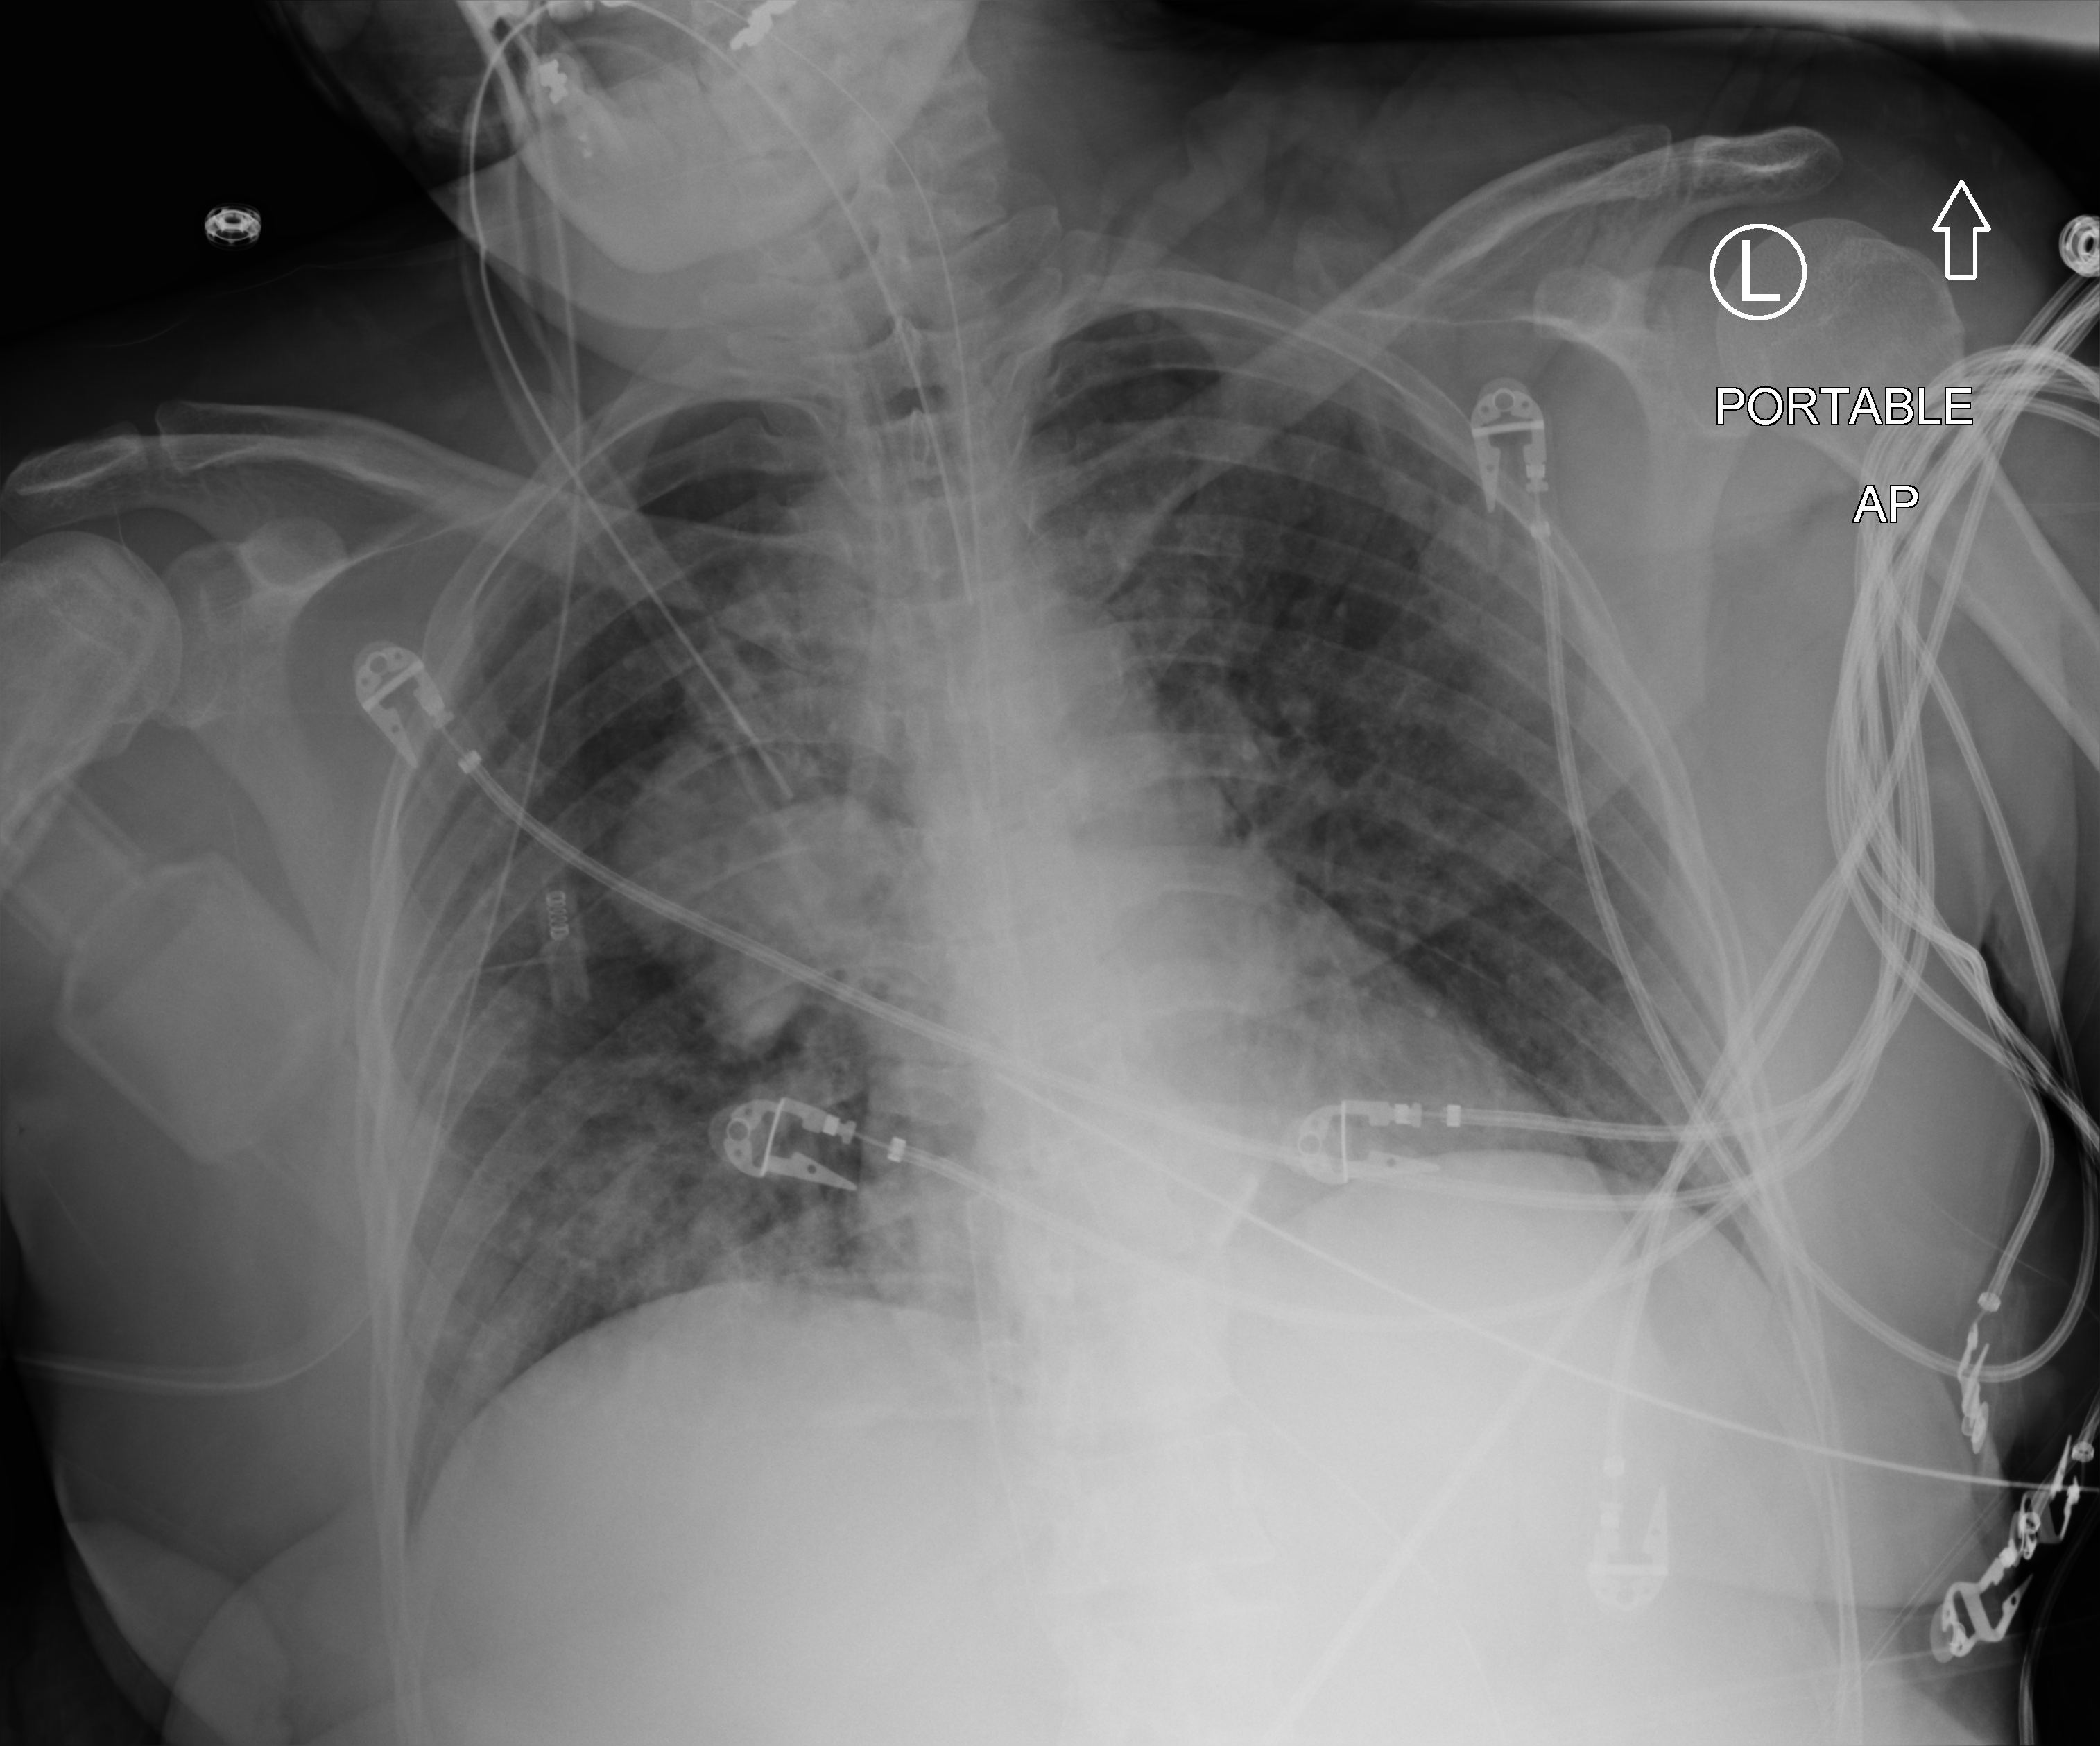
Chest X-ray (portable), anteroposterior (AP) projection. Patient hospitalised with COVID-19; female, aged 18–59 years.
Admission-level facts for this patient (not findings on this image; timing relative to this image not recorded):
- length of hospital stay: 22 days
- mechanically ventilated during this hospital stay: yes
- diabetes (admission record): no